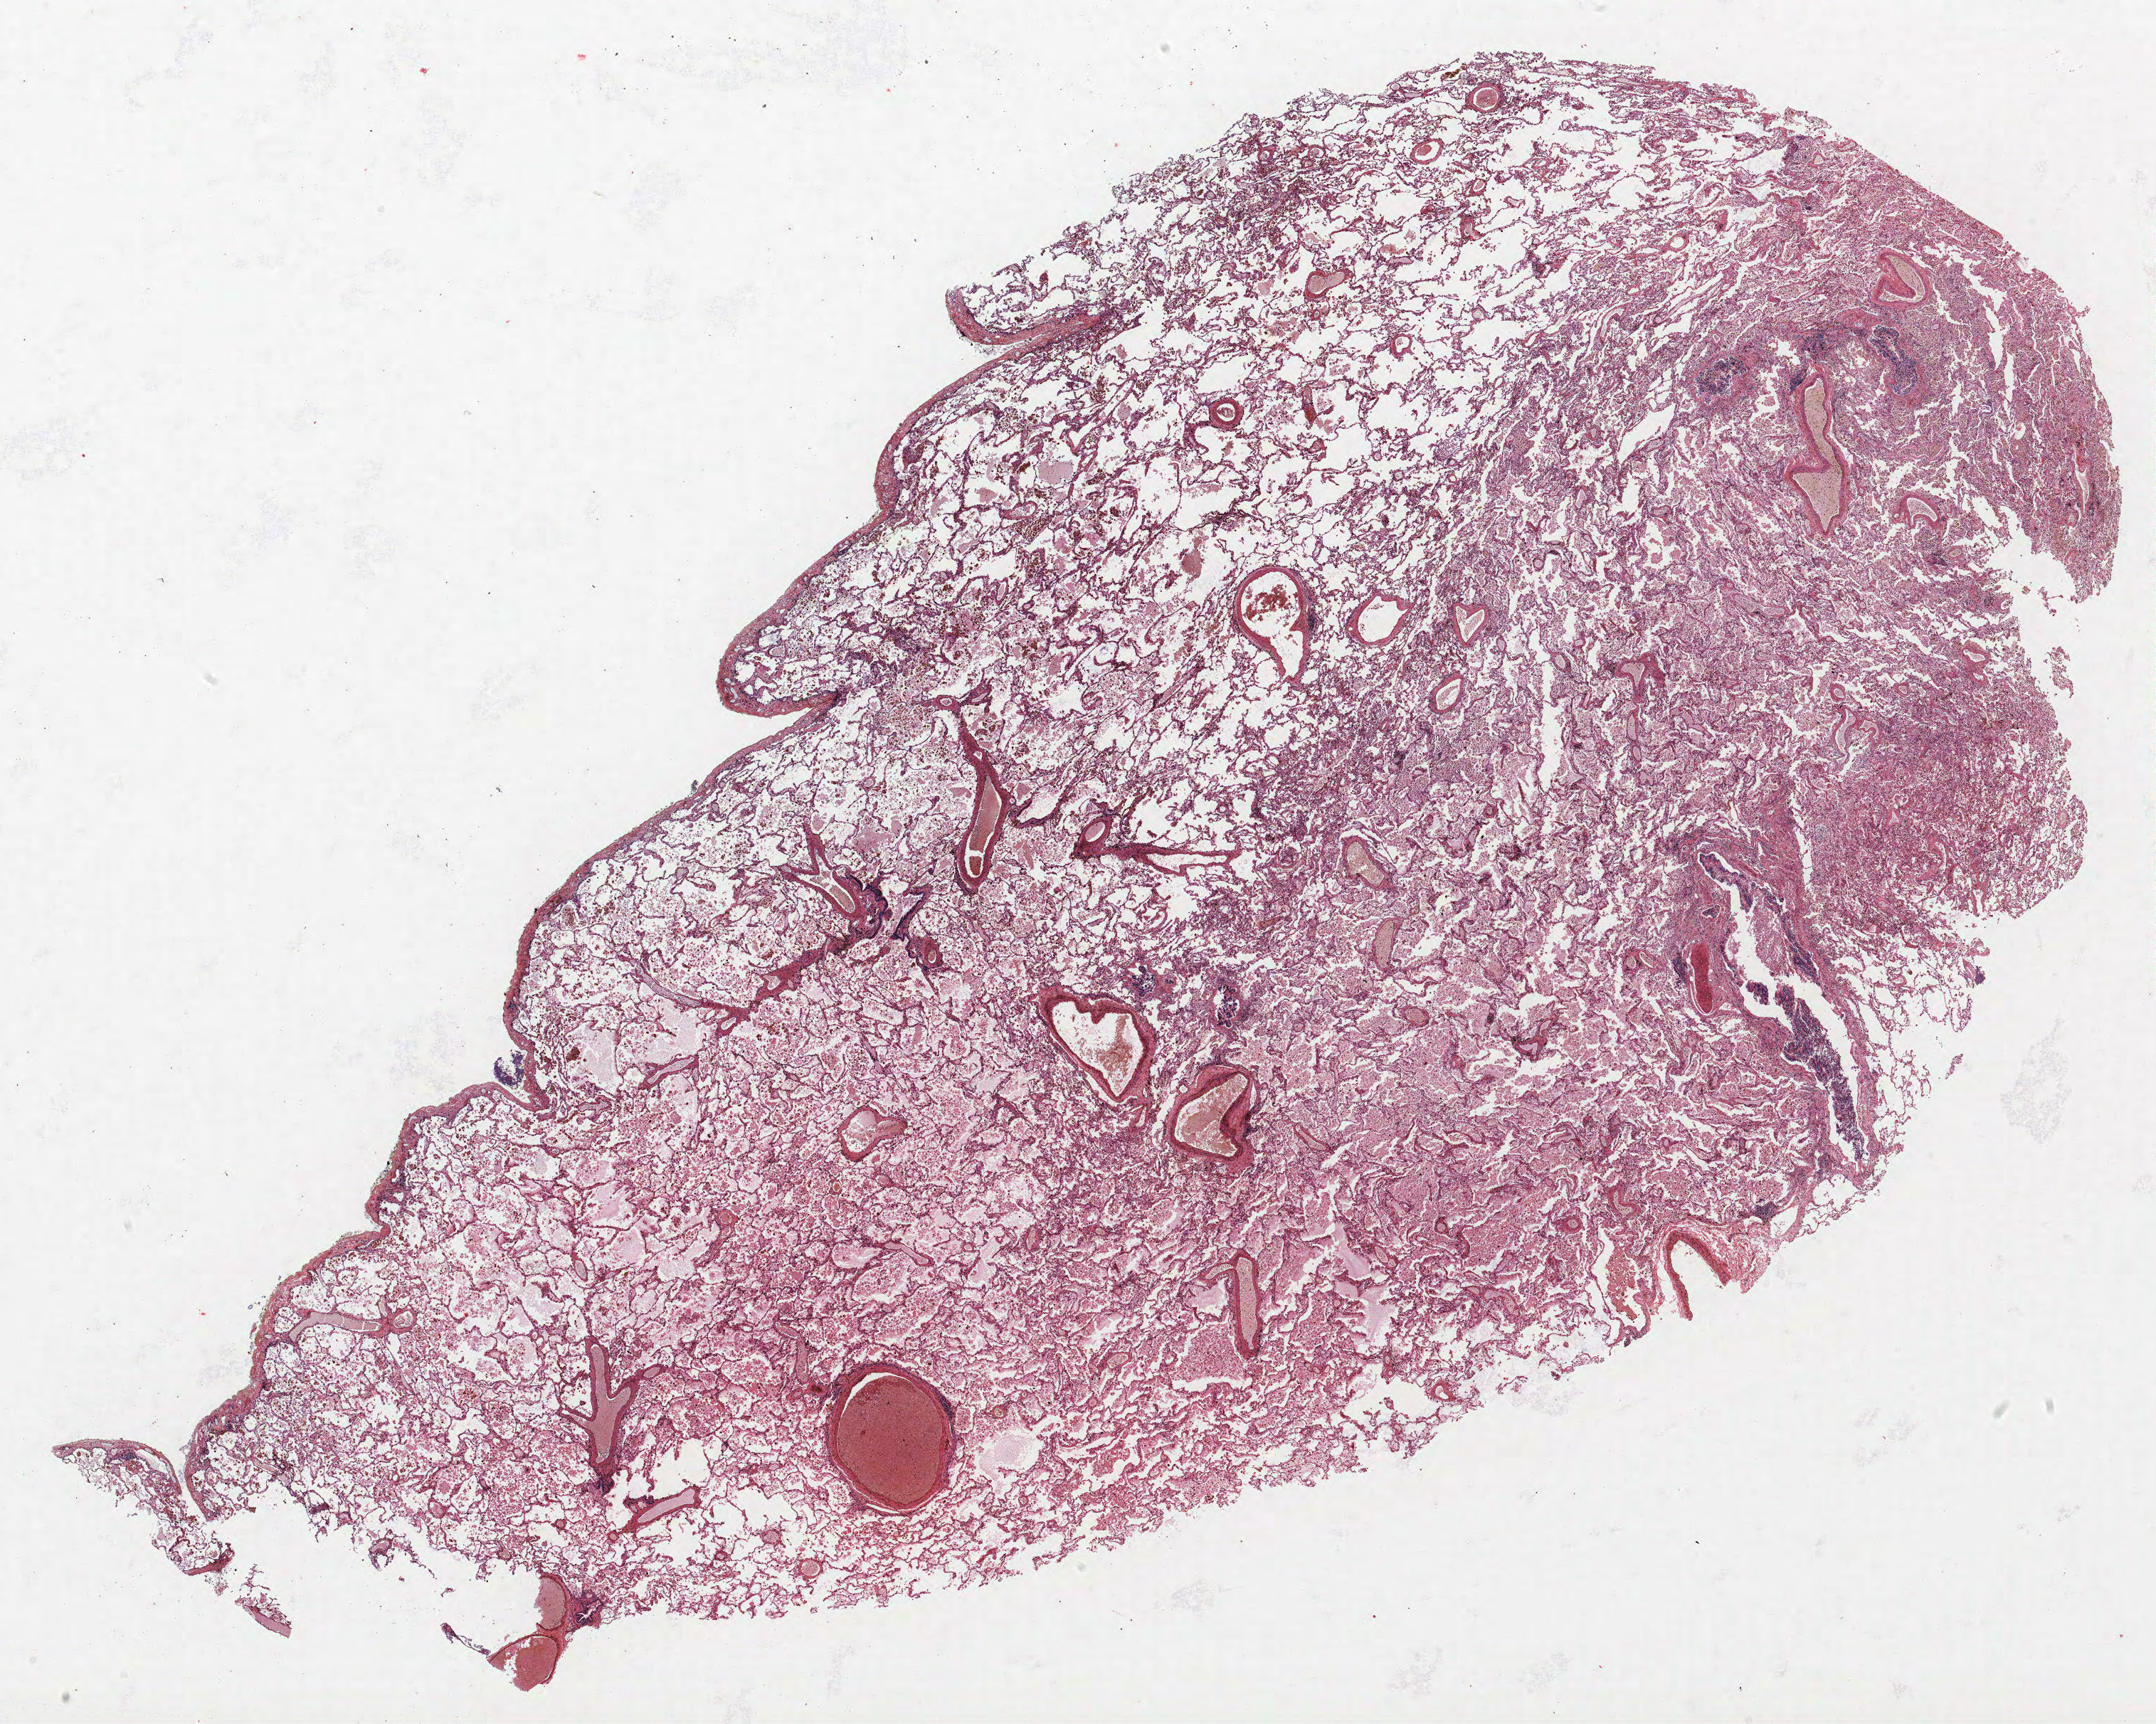
Hematoxylin and eosin (H&E) stained whole-slide image — shown as a low-resolution overview of the whole scanned area (about 24.2 x 19.4 mm, slide scanned at 40x); FFPE section; lung. Male, age 56 at enrolment. Current smoker at enrolment. Grade: poorly differentiated (G3).
• tumour size (pathology): 60 mm
• stage (AJCC 6th edition): IIB
• primary tumour location (clinical record): right upper lobe
• participant's lung-cancer diagnosis: Adenocarcinoma, NOS (ICD-O-3 8140/3)